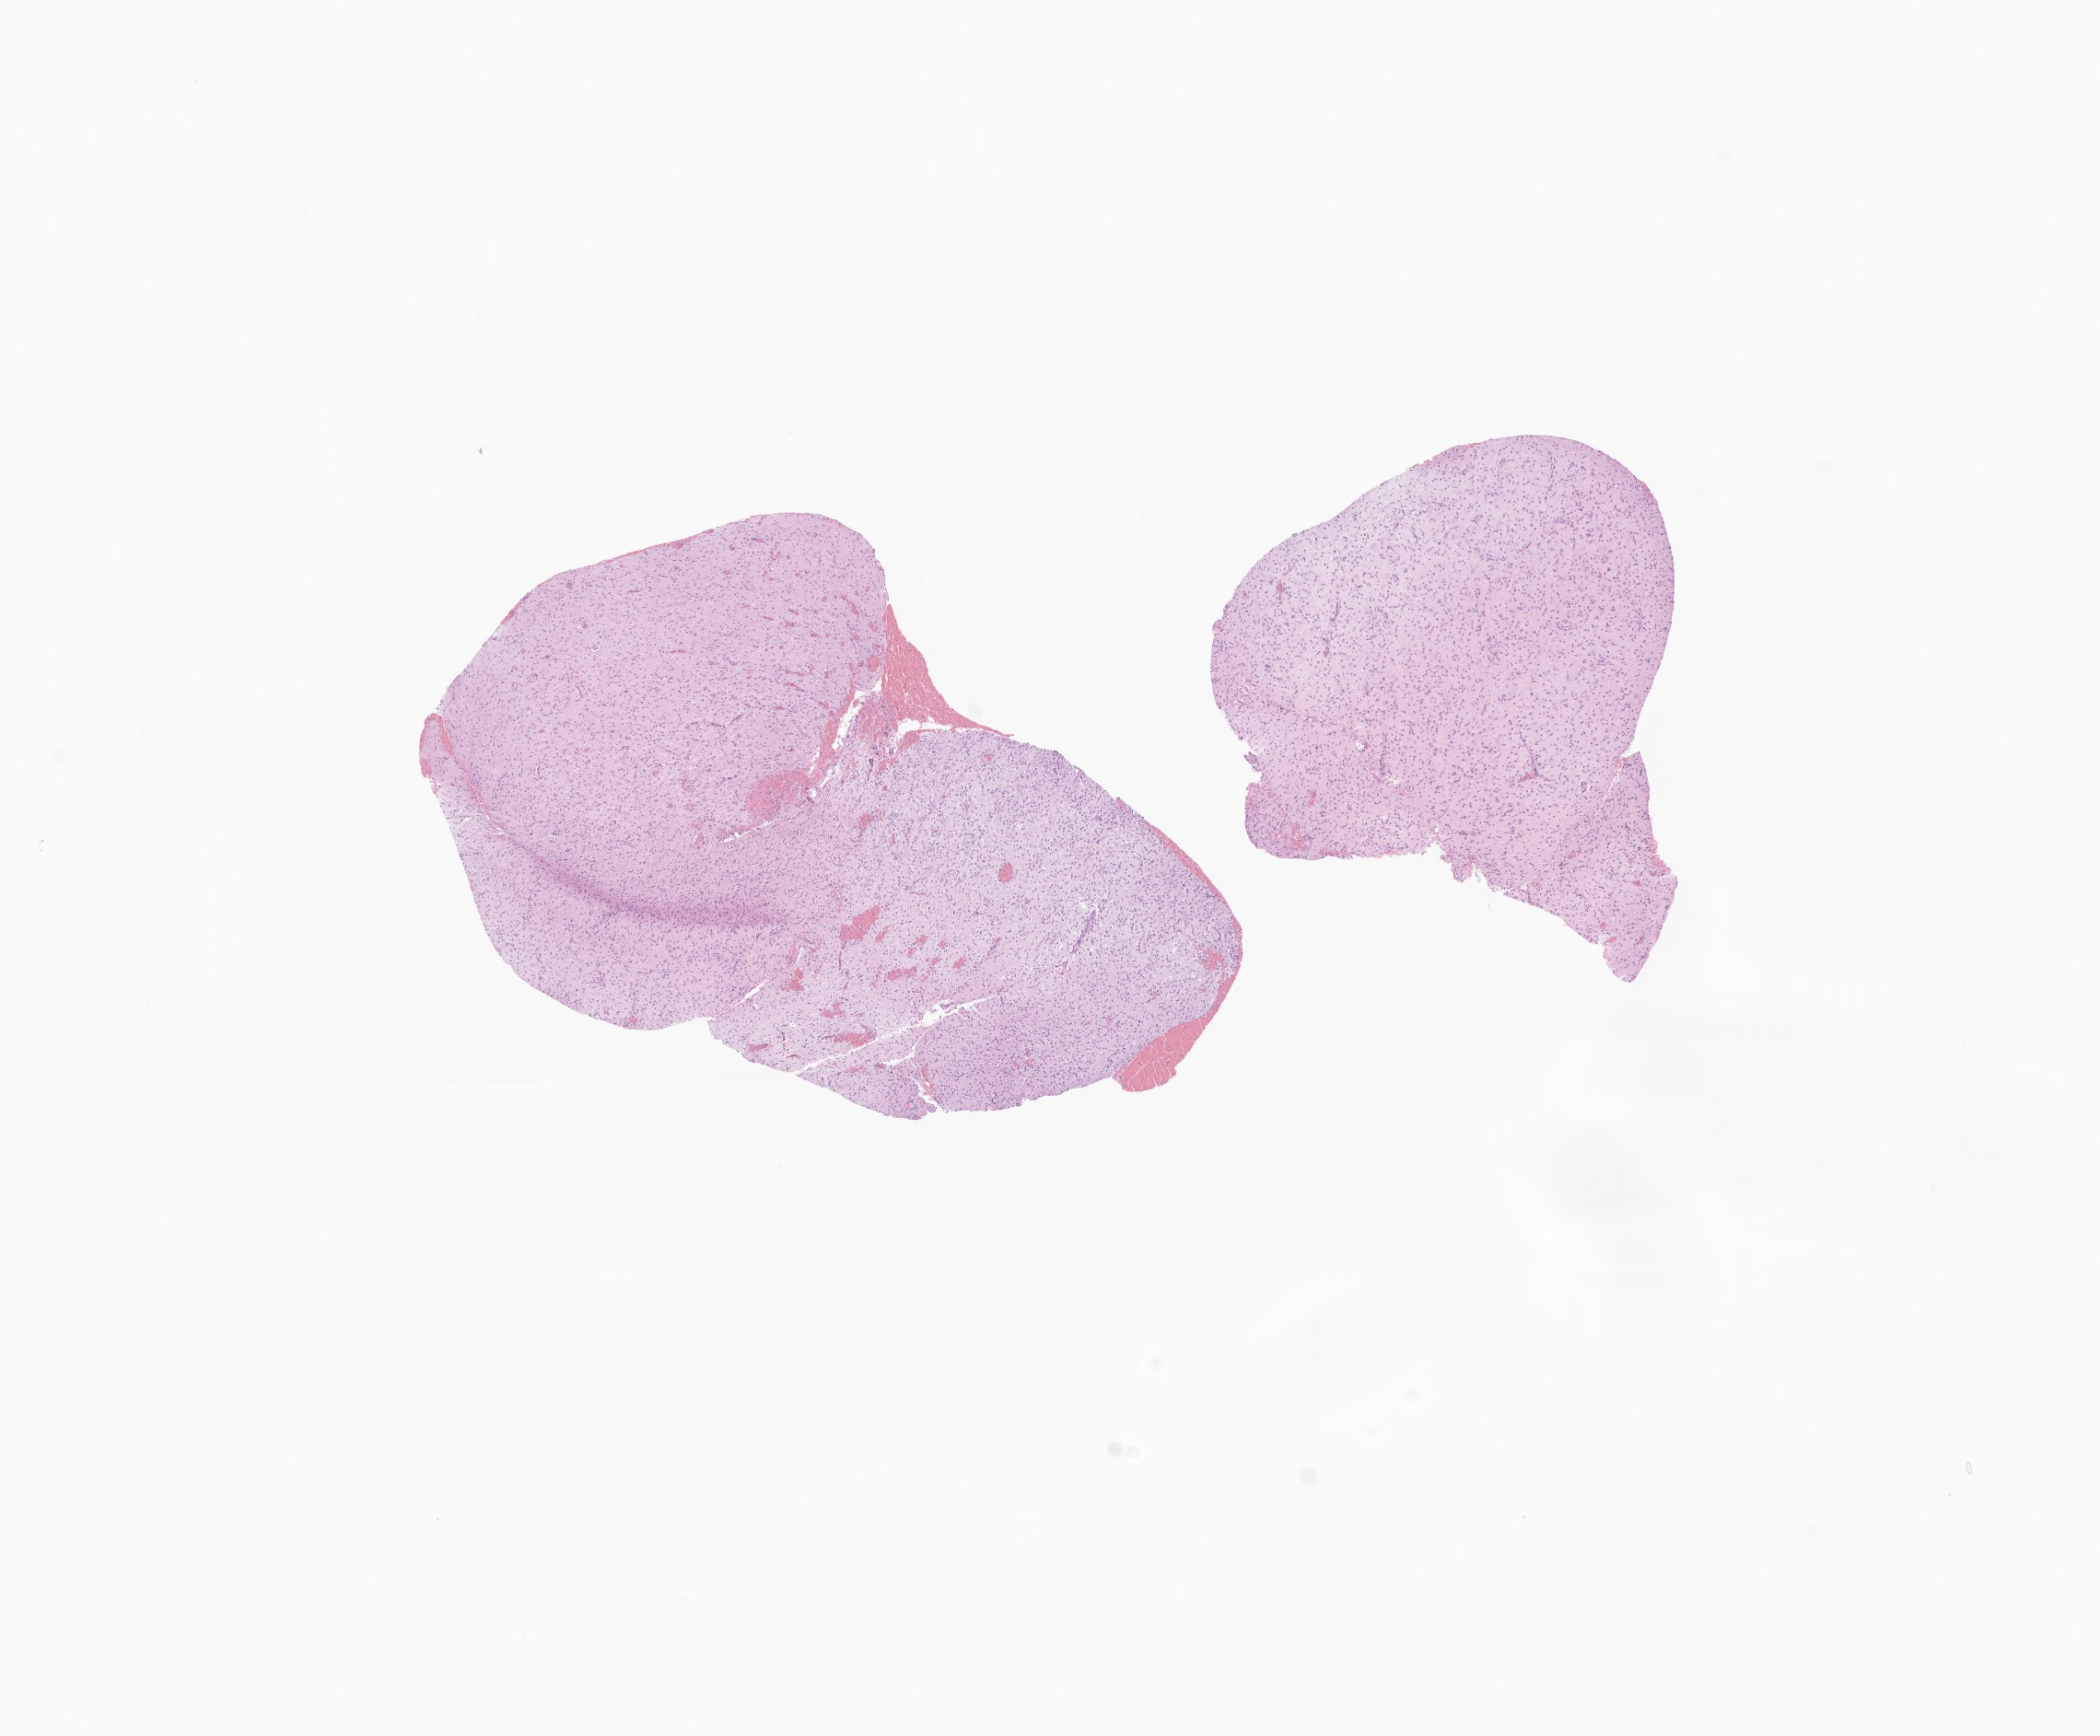
H&E whole-slide image of tumor tissue from the temporal lobe, low-resolution overview of the scanned area, about 9.6 x 7.9 mm, FFPE section. Patient male; age 346 days.
Recorded diagnosis: Neoplasm, malignant, uncertain whether primary or metastatic.